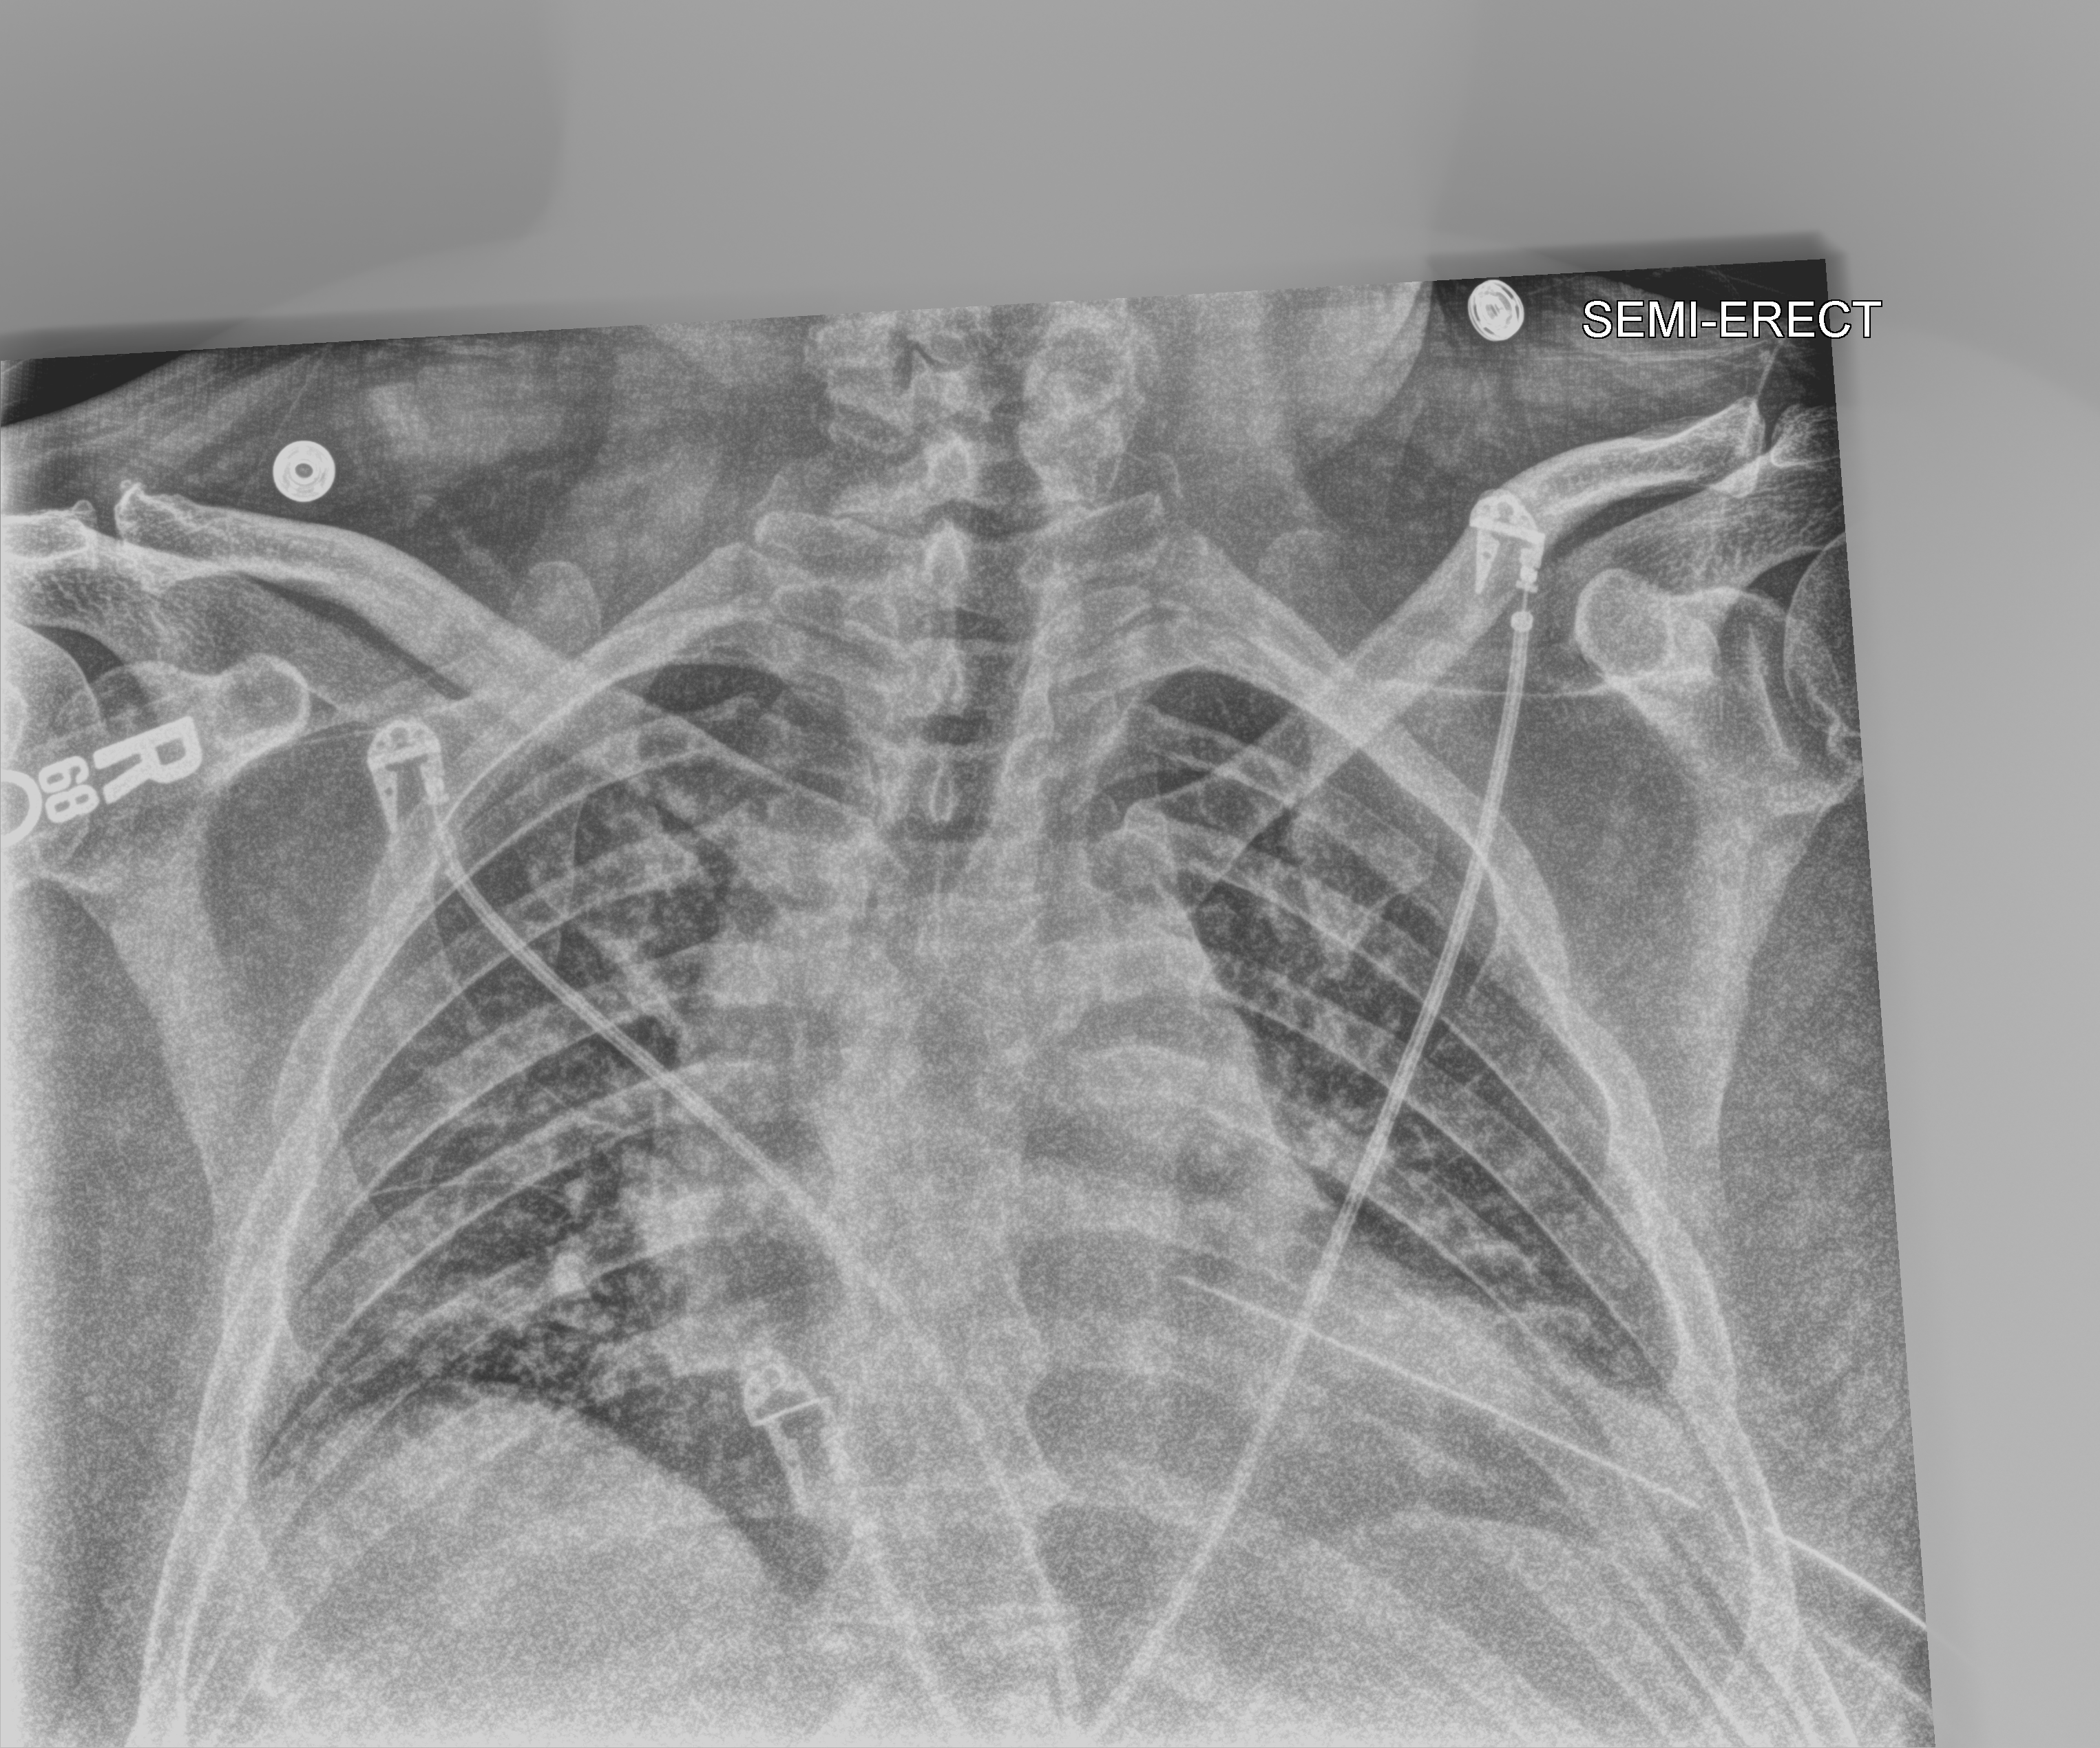
Bedside chest radiograph (computed radiography). Patient hospitalised with COVID-19; male, aged 18–59 years.
Admission-level facts for this patient (not findings on this image; timing relative to this image not recorded): mechanically ventilated during this hospital stay: no; admitted to intensive care during this hospital stay: no.